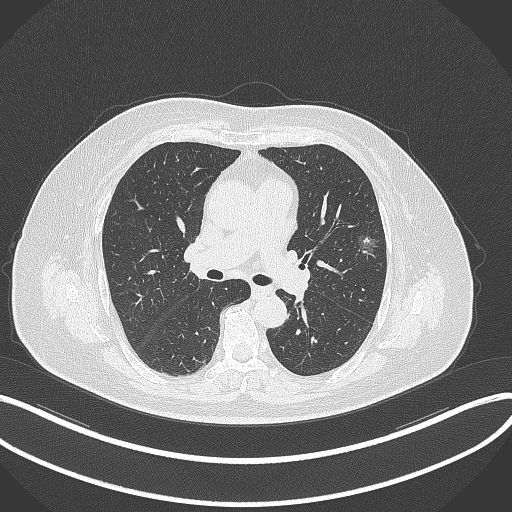
Chest CT, one axial slice. Slice 213 of 315 in the series (ordered by position). Reconstruction kernel B70f. Lung window (W 1500 / L -600 HU). 512 × 512 image matrix, field of view 400 × 400 mm. Female patient, age 76 years. Case-level facts recorded for this patient, not image findings: clinical TNM (as recorded): T1b N0 M0; histopathological grade: G1-2.
Outlined on this slice (bounding box drawn by a radiologist):
- lung tumour (recorded histology: adenocarcinoma): bounding box (x1, y1, x2, y2) in pixels: (357, 228, 381, 257)